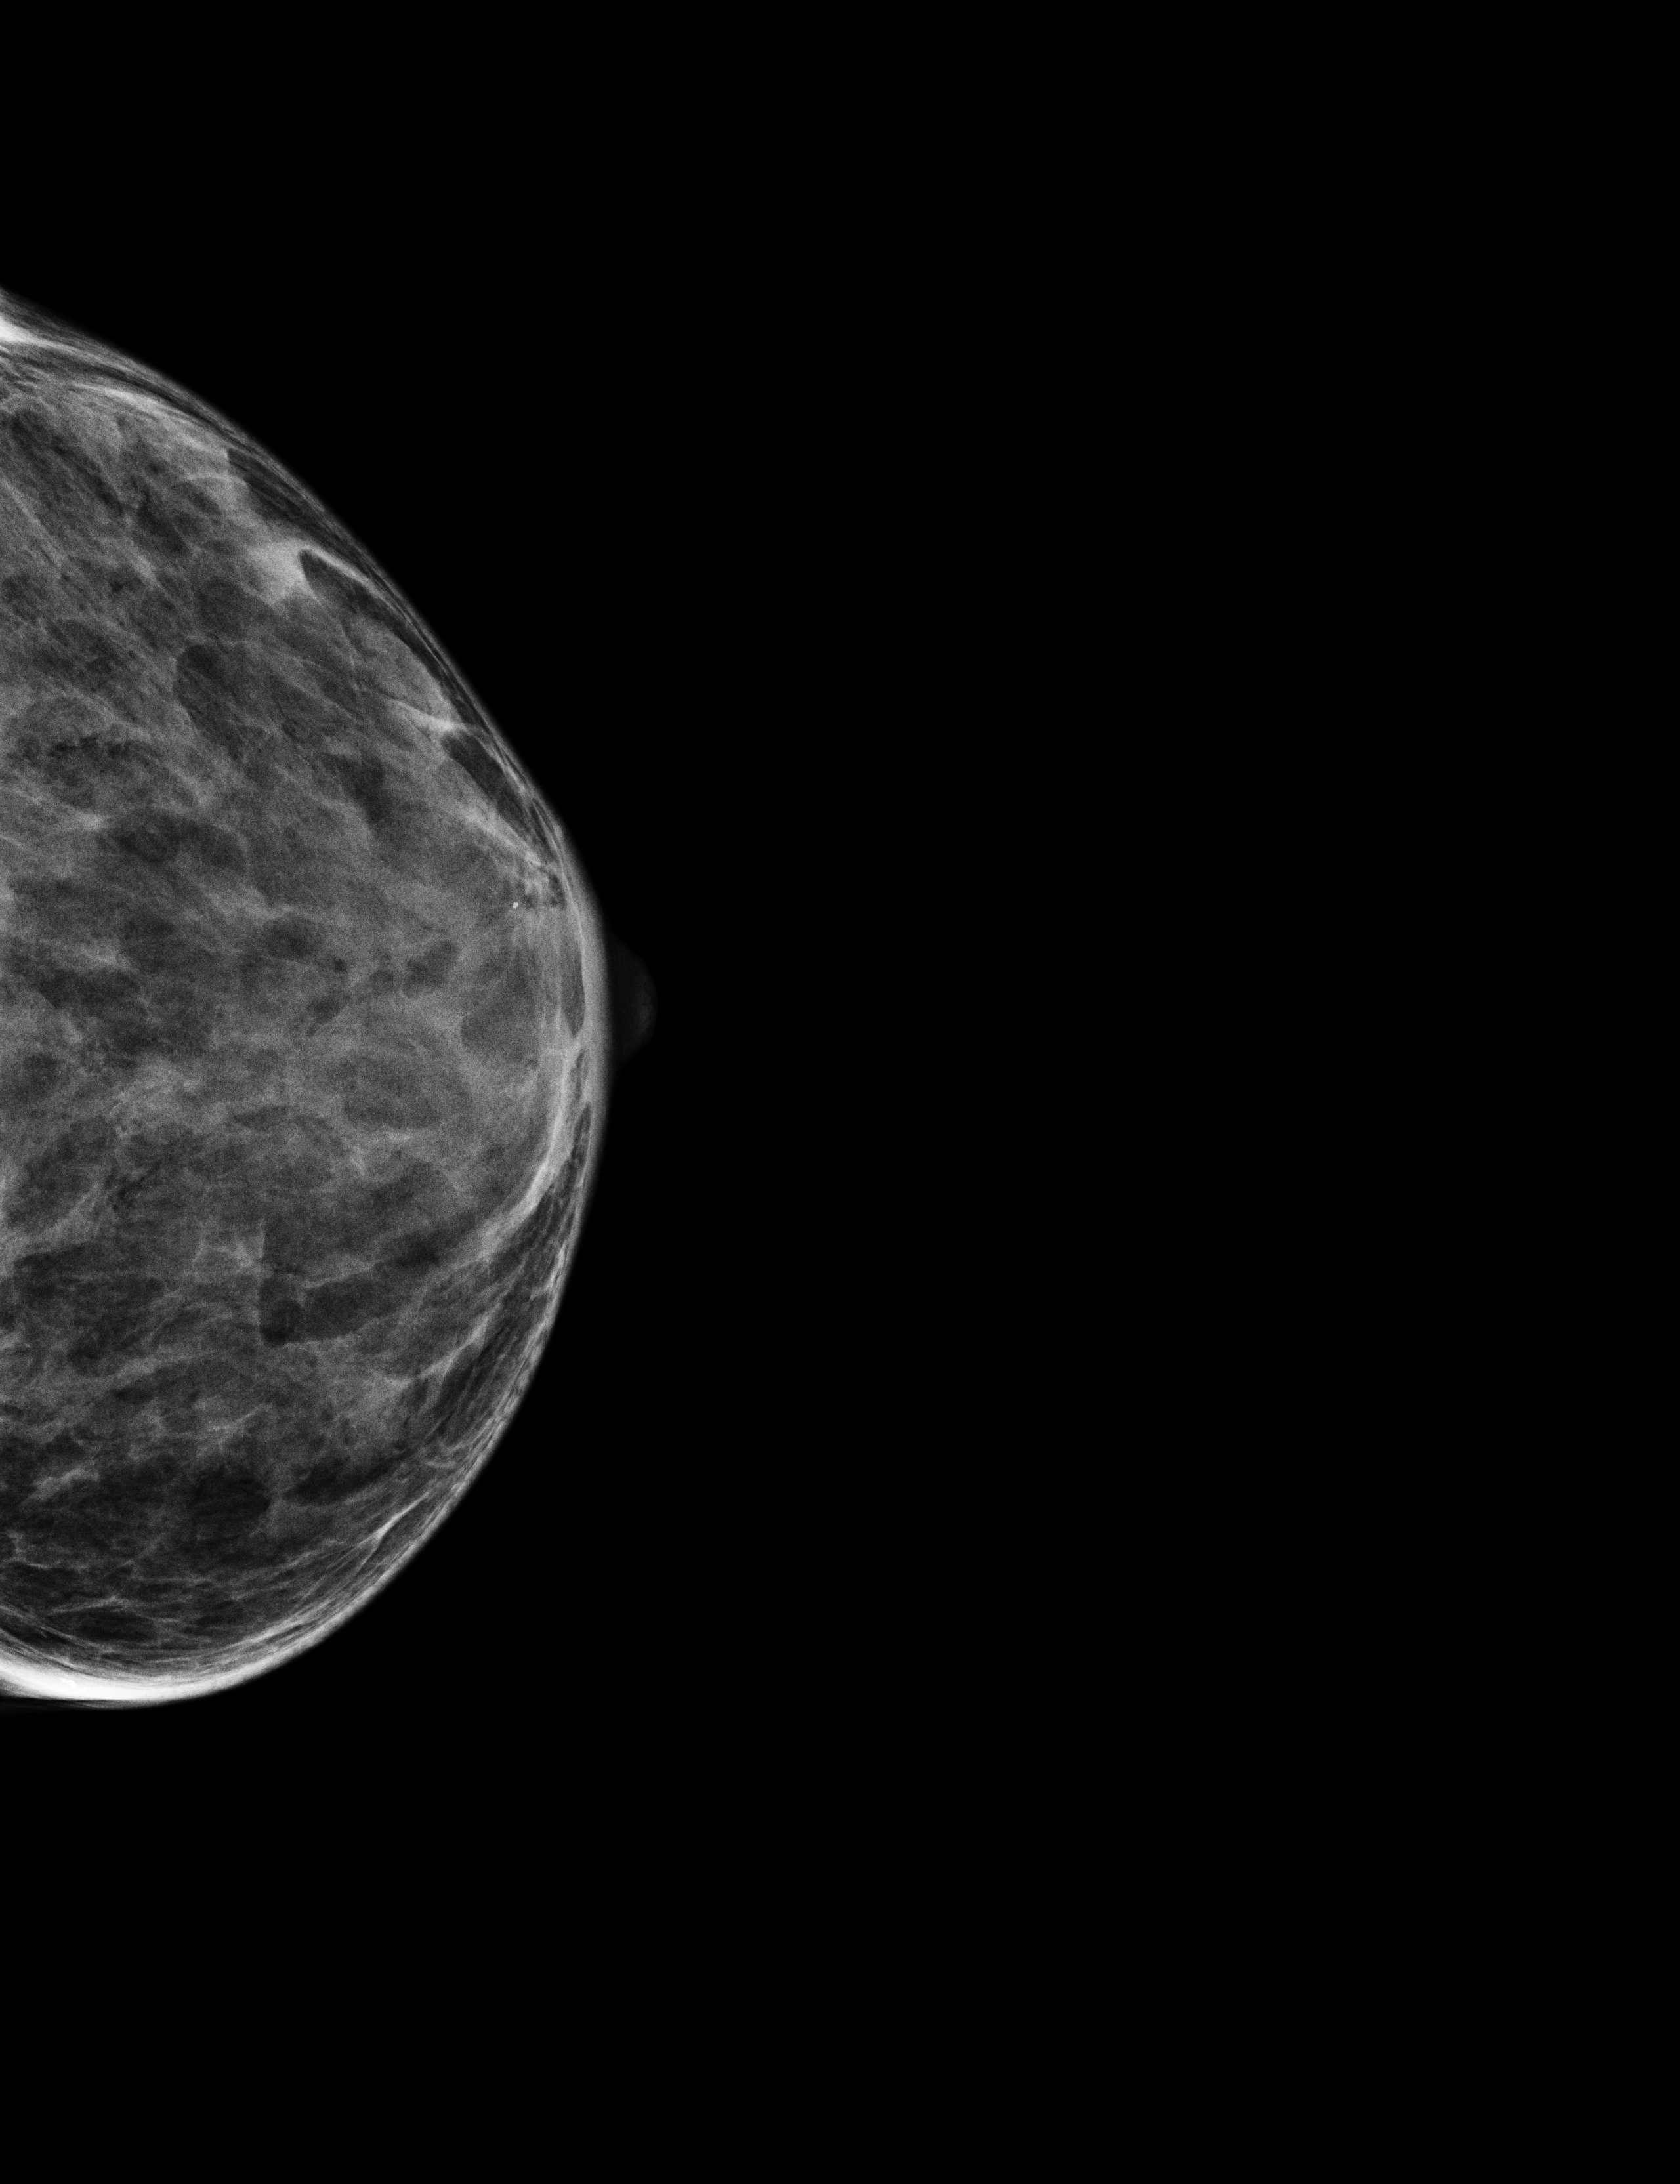
Annual screening mammography examination, compressed breast thickness 20 mm, system: Selenia Dimensions. Patient aged 69 years (female).
Image type: full-field digital mammogram. Breast: left. Projection: CC view.